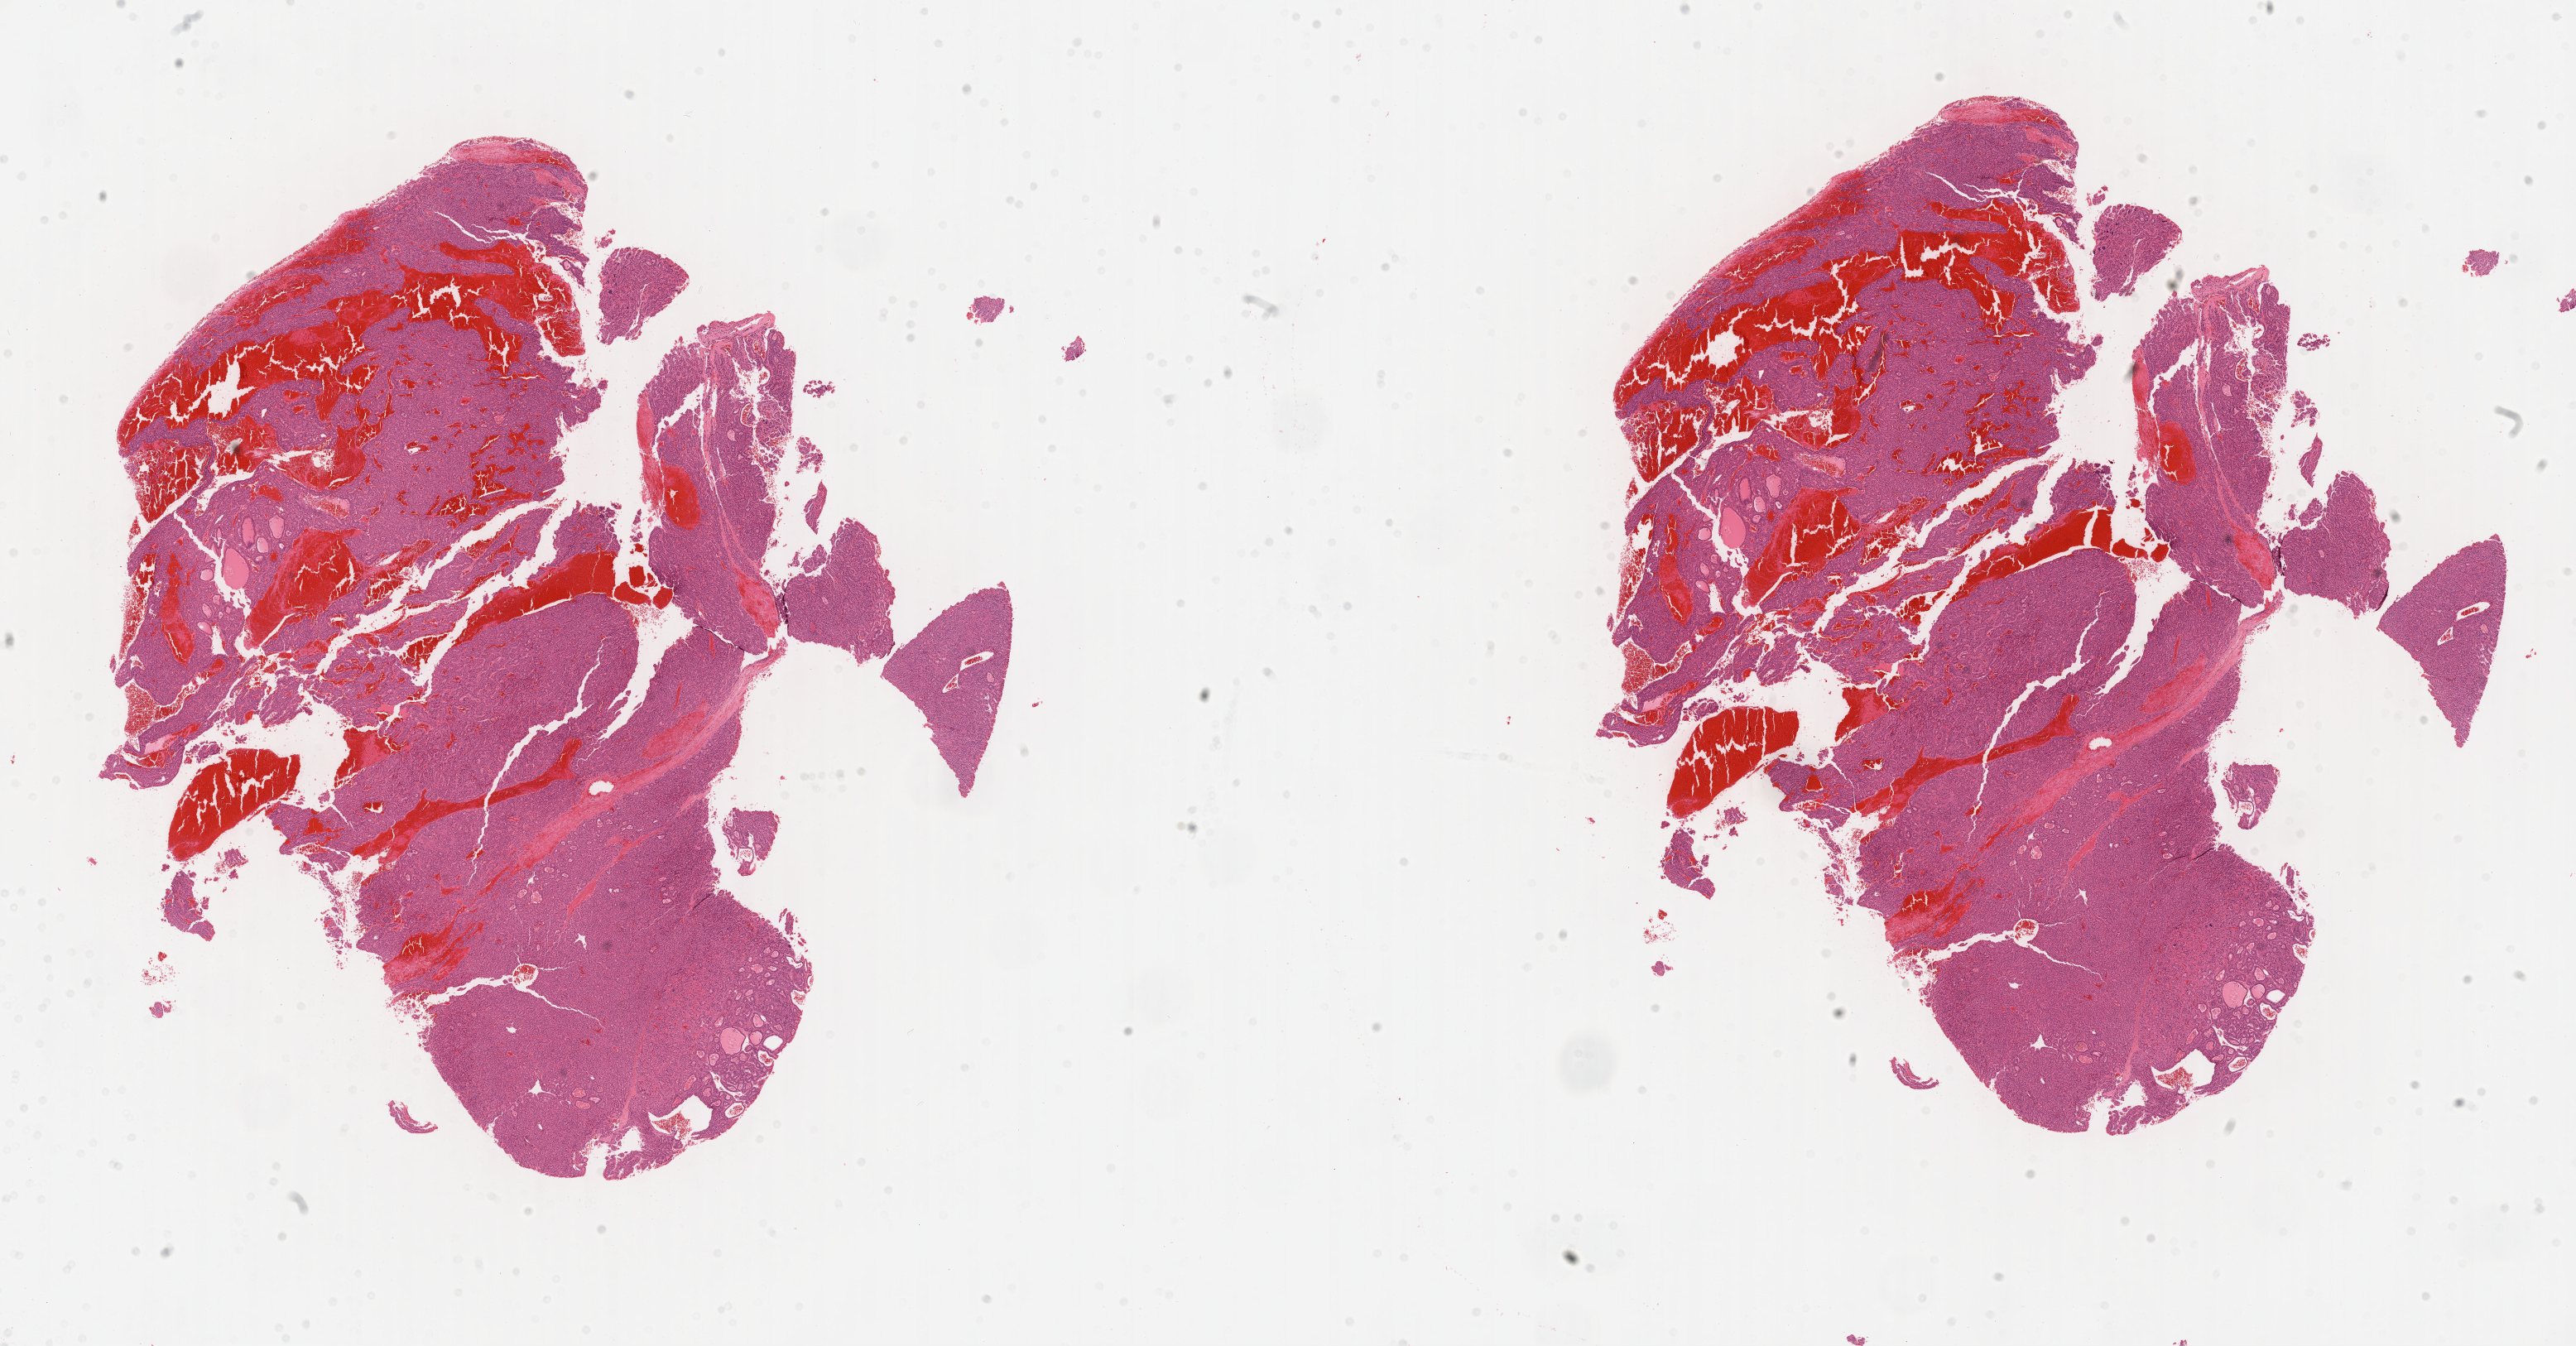
H&E-stained whole-slide image — low-resolution overview of the scanned area, about 25.1 x 13.1 mm (slide scanned at 40x), FFPE section, liver, primary tumour sample. Male, age 68 years at initial diagnosis. Histologic grade: G3 (poorly differentiated).
AJCC pathologic stage: I (6th edition). Histologic diagnosis: Hepatocellular carcinoma, NOS.